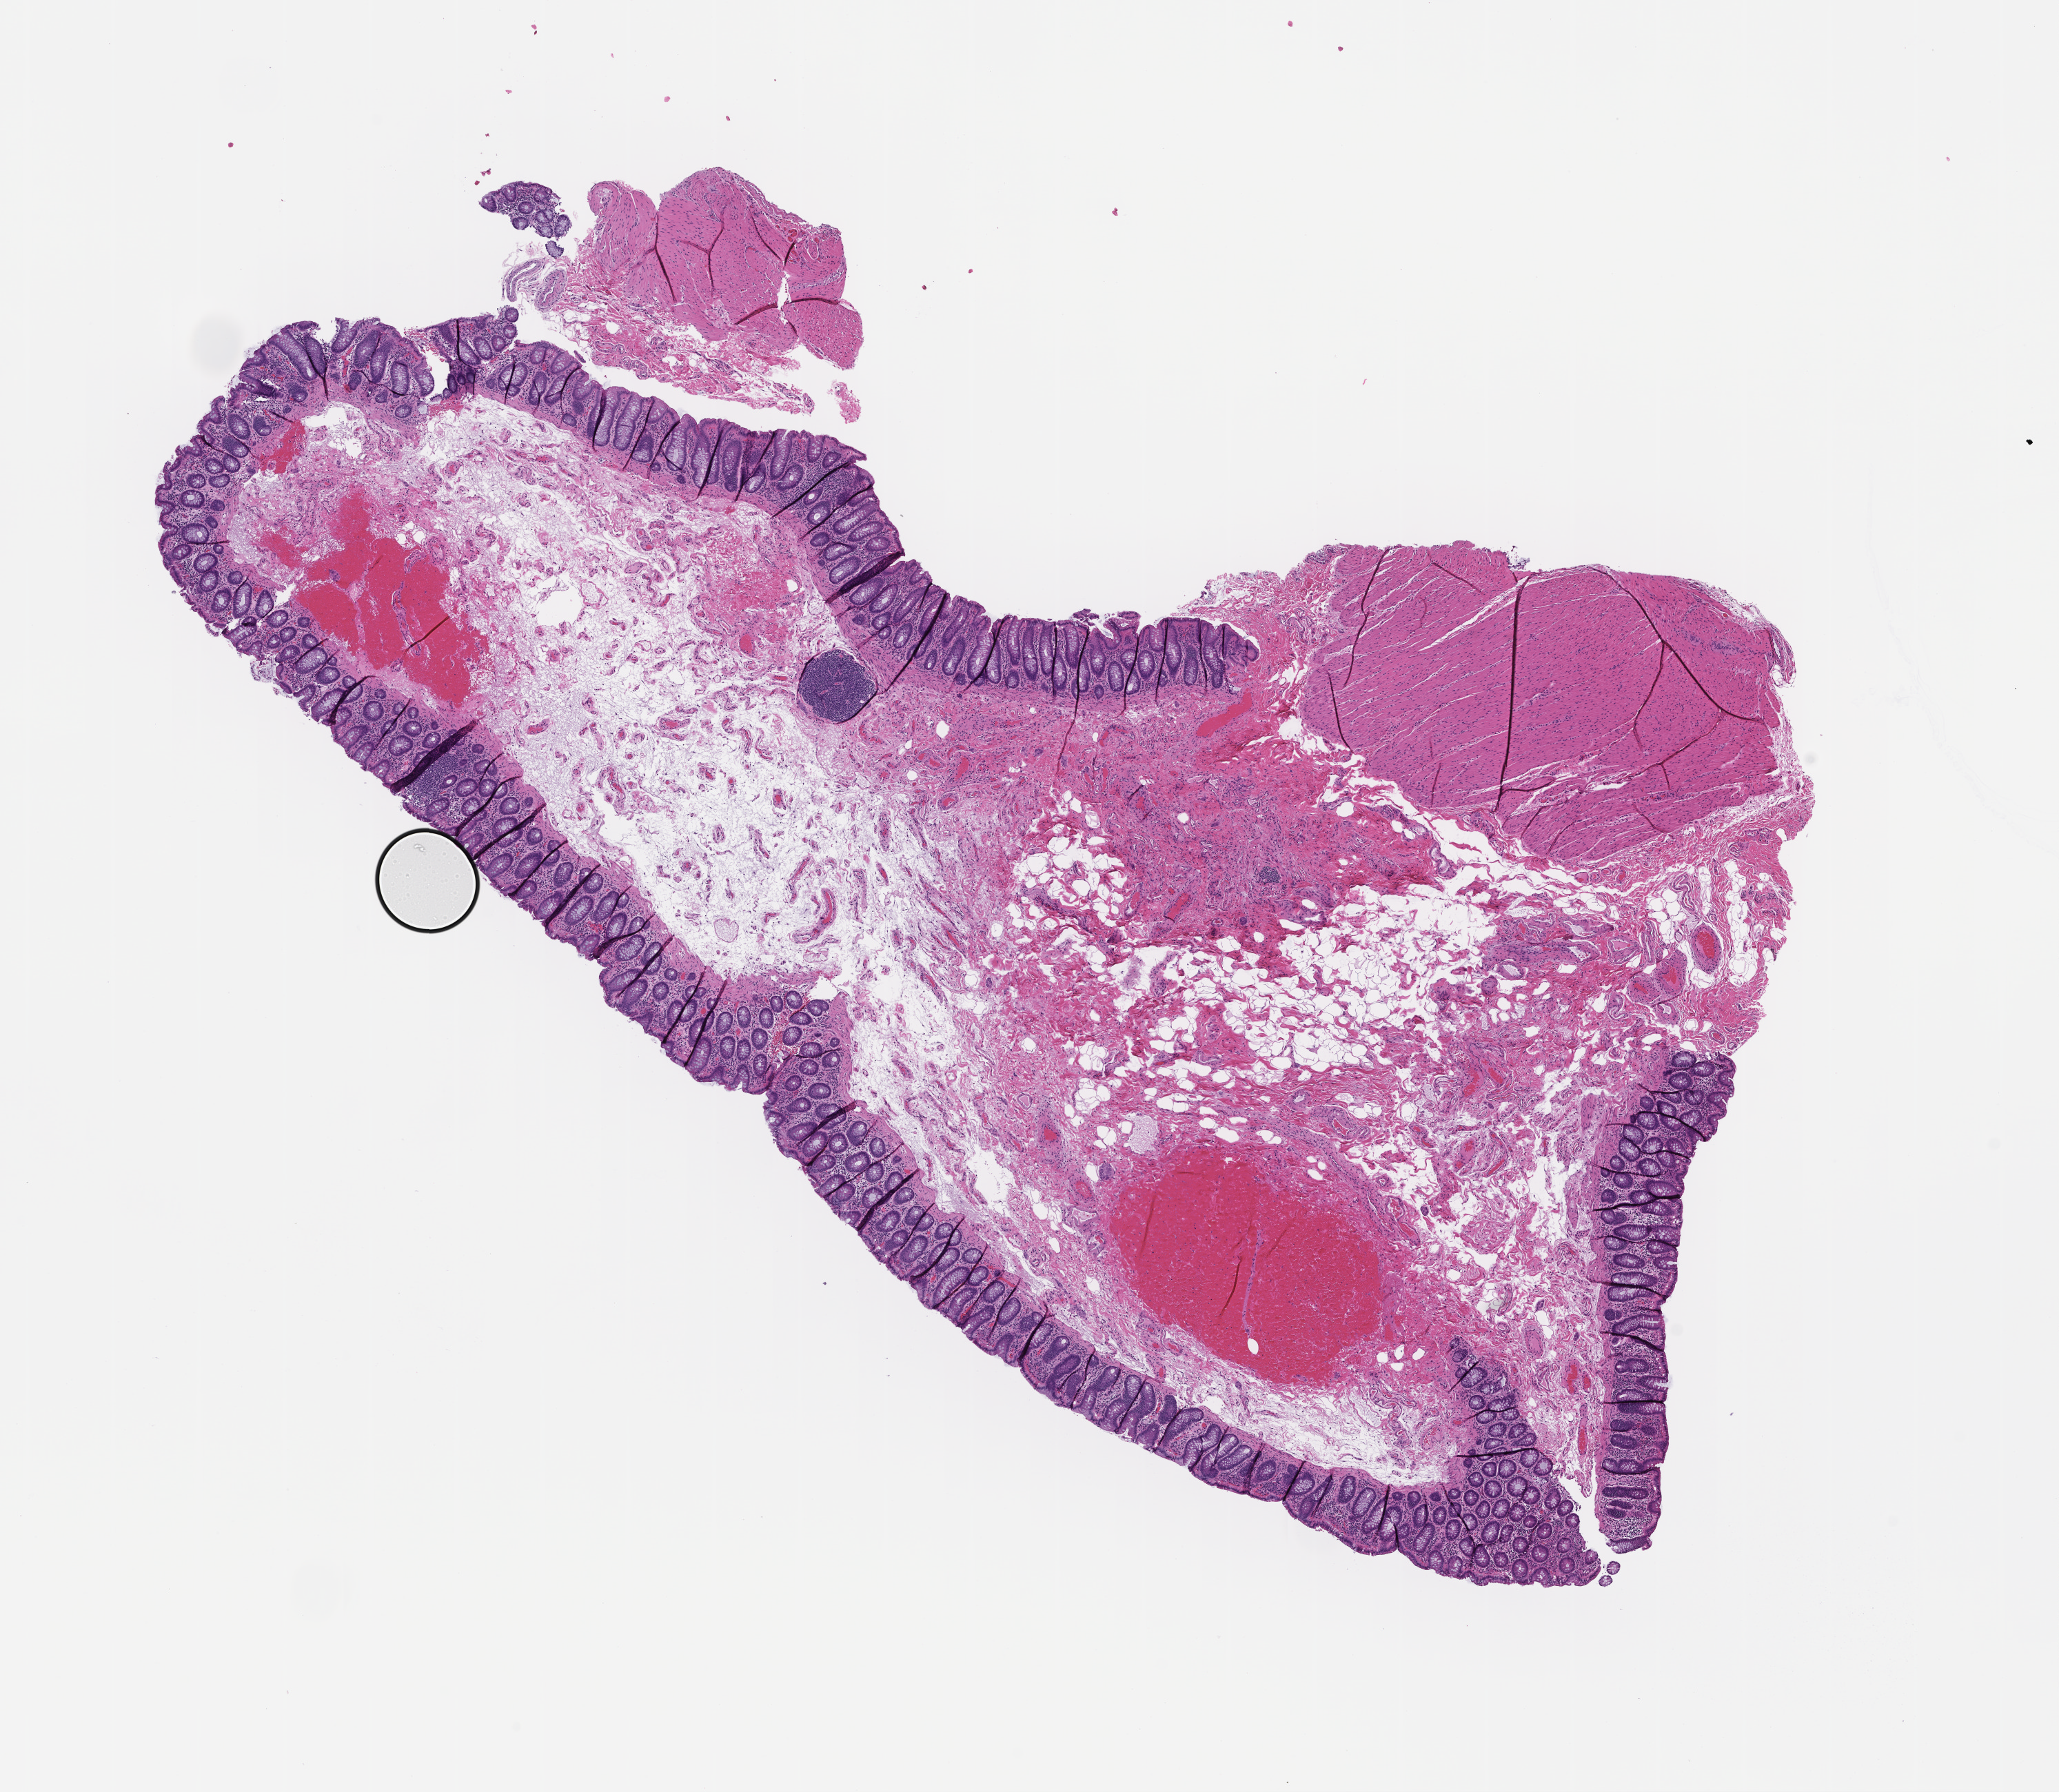
Digitized haematoxylin and eosin-stained section, shown as a low-resolution overview of the whole scanned area (about 12.1 x 10.5 mm), formalin-fixed, paraffin-embedded (FFPE) tissue. Female patient.
This section: metastasis (sampled organ not recorded). Patient diagnosis (primary): Colorectal Carcinoma.